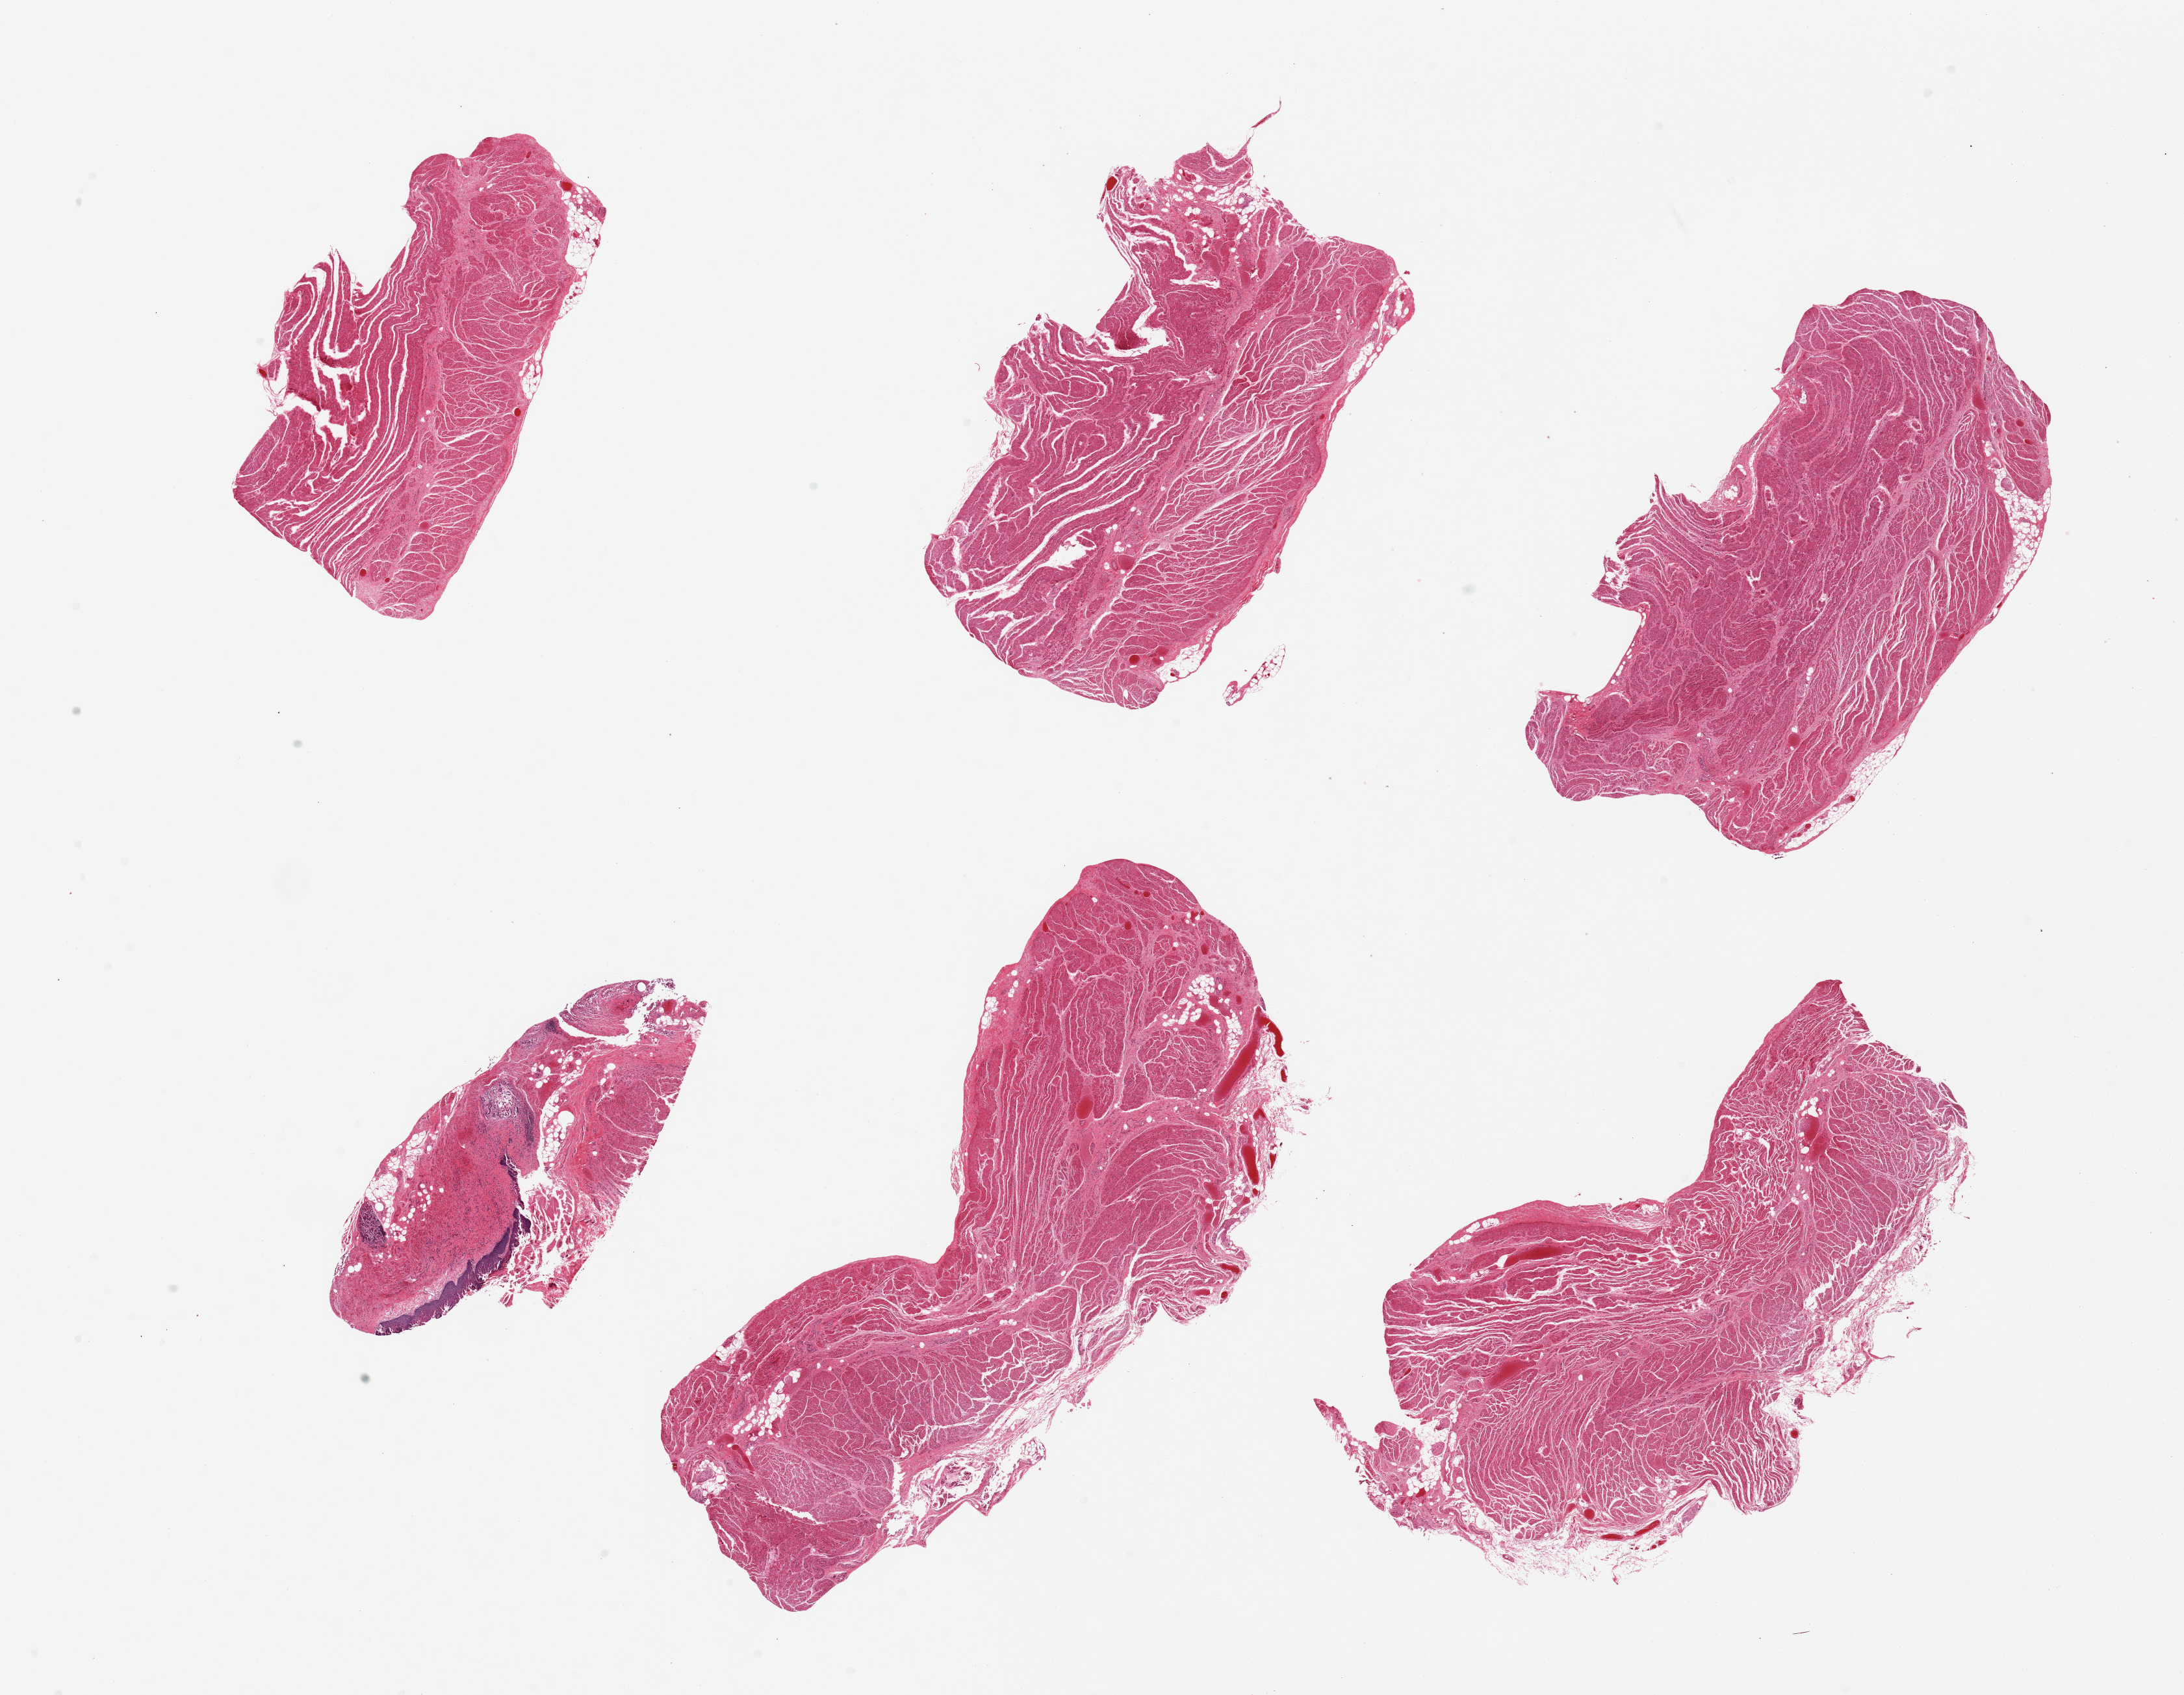
Hematoxylin and eosin (H&E) whole-slide image, brightfield, a low-resolution overview of the entire scanned area, about 26.6 x 20.6 mm; PAXgene-fixed, paraffin-embedded tissue; sampled site (target tissue): gastroesophageal junction; tissue donor sample. Male donor.
Pathologist's review note for this sample: 6 pieces. one piece has surface epithelium and submucosal glands: not targets.